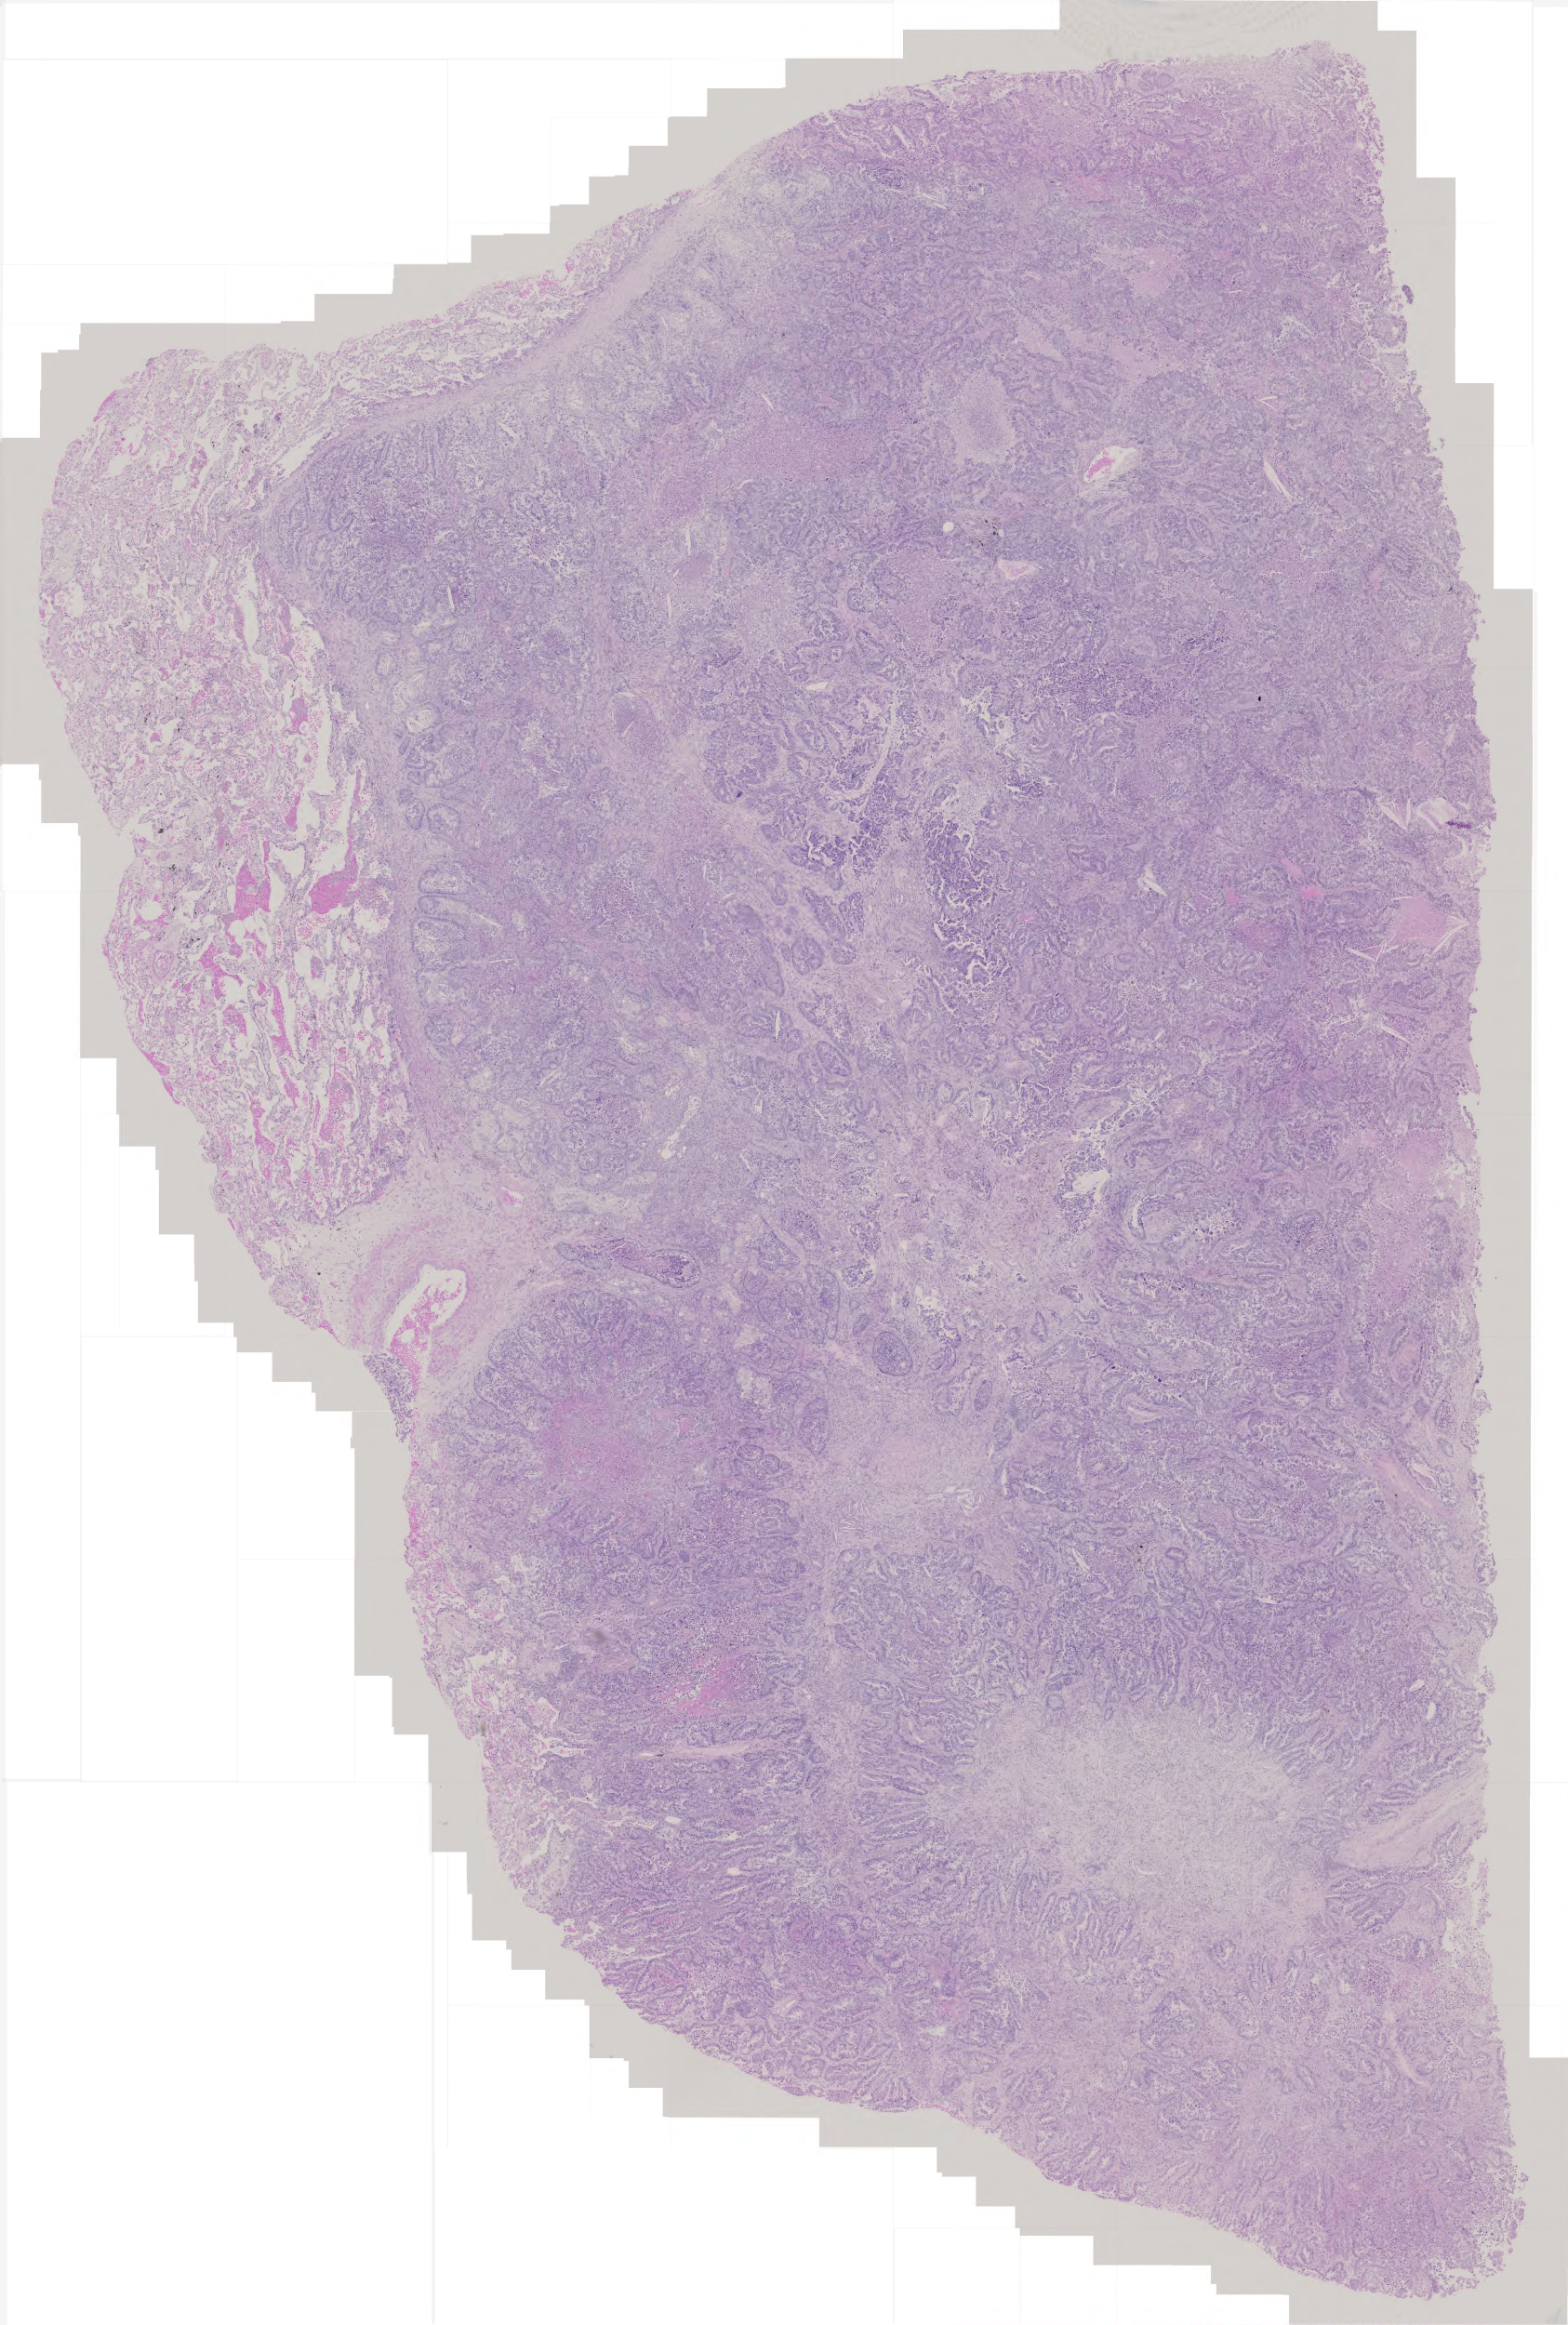
H&E whole-slide image — a low-resolution overview of the entire scanned area, about 3.4 x 5.0 mm, formalin-fixed paraffin-embedded (FFPE) diagnostic section, lung, primary tumour sample. Patient: female, age at initial diagnosis 58 years.
Histologic diagnosis: Adenocarcinoma with mixed subtypes (upper lobe, lung). Laterality: right. AJCC pathologic stage: IB (5th edition).